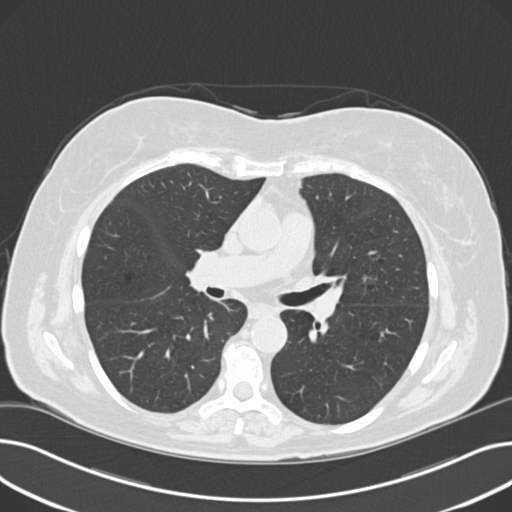
Low-dose screening chest CT, axial slice; third screening round (two years after baseline); lung window (W 1500 / L -600 HU); standard (soft-tissue) reconstruction kernel (B30f); 512 × 512 image matrix, field of view 372 × 372 mm. Female, age 60 years at enrolment. Current smoker at enrolment.
• Lesion marked by an expert reader, bounding box <355,267,393,298> (left, top, right, bottom; pixels).
• The screening reader recorded 8 non-calcified nodules or masses ≥4 mm on this exam; which of them this box marks is not recorded.
• Later outcome: lung cancer diagnosed 176 days after this screen — non-small cell carcinoma, left upper lobe, poorly differentiated (G3), stage IB (AJCC 6th edition), 7 mm at pathology.